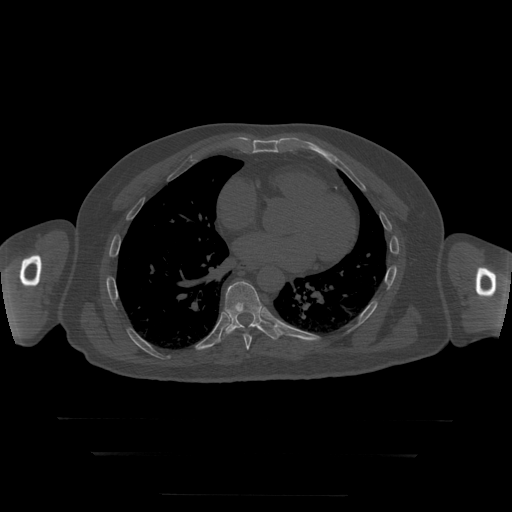
CT including the spine, one axial slice. Slice 152 of 397 in the series (ordered by position). 120 kVp. Bone window (W 1800 / L 400 HU). 1.25 mm slice thickness. 512 × 512 image matrix. Patient age 73 years. Case-level facts recorded for this patient, not image findings: primary cancer: prostate.
Annotated regions visible in this slice (semi-automatic segmentation, software-assisted and operator-edited):
- T8 vertebra: bounding box <244,334,252,350> (left, top, right, bottom; pixels)
- T9 vertebra: <220,282,281,342>